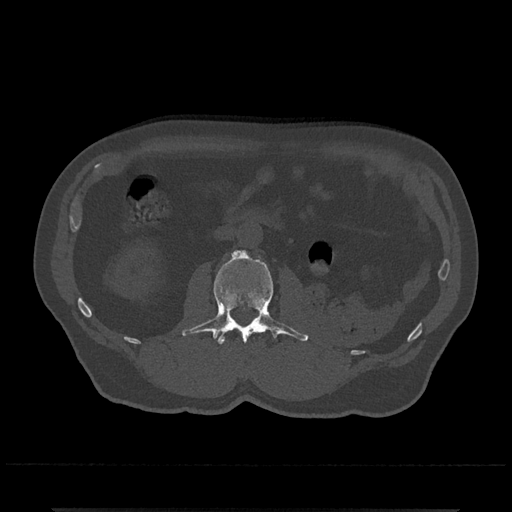
CT including the spine, one axial slice. Slice 294 of 797 in the series (ordered by position). Bone window (W 1800 / L 400 HU). 512 × 512 image matrix, field of view 393 × 393 mm. Patient: male, 67 years. Case-level facts recorded for this patient, not image findings: primary cancer: prostate.
Structures marked on this image (semi-automatic segmentation, software-assisted and operator-edited):
- L2 vertebra: bounding box [x1, y1, x2, y2] px = [181, 249, 309, 344]